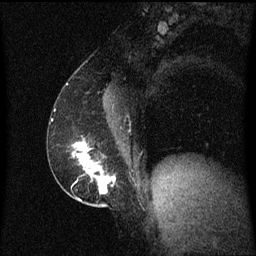
Breast MRI (dynamic contrast-enhanced), one sagittal slice. Dynamic contrast-enhanced series, image 2 of 3 at this slice position (ordered by acquisition). 1.5 T. TE 4.2 ms, TR 8.4 ms. 256 × 256 image matrix. Female patient, age 52 years. From the clinical record (not read from this slice): setting: breast cancer imaged before/during neoadjuvant chemotherapy; receptor status: HER2-positive.
Structures marked on this image (semi-automatically segmented with operator editing):
- analysis volume of interest (the breast-tissue region the enhancement analysis was run in; not a lesion): box from (x=62, y=136) to (x=119, y=203) px
- tumour enhancement mask (voxels above the 70 % enhancement threshold inside the analysis volume of interest): (x=74, y=142)–(x=116, y=195)